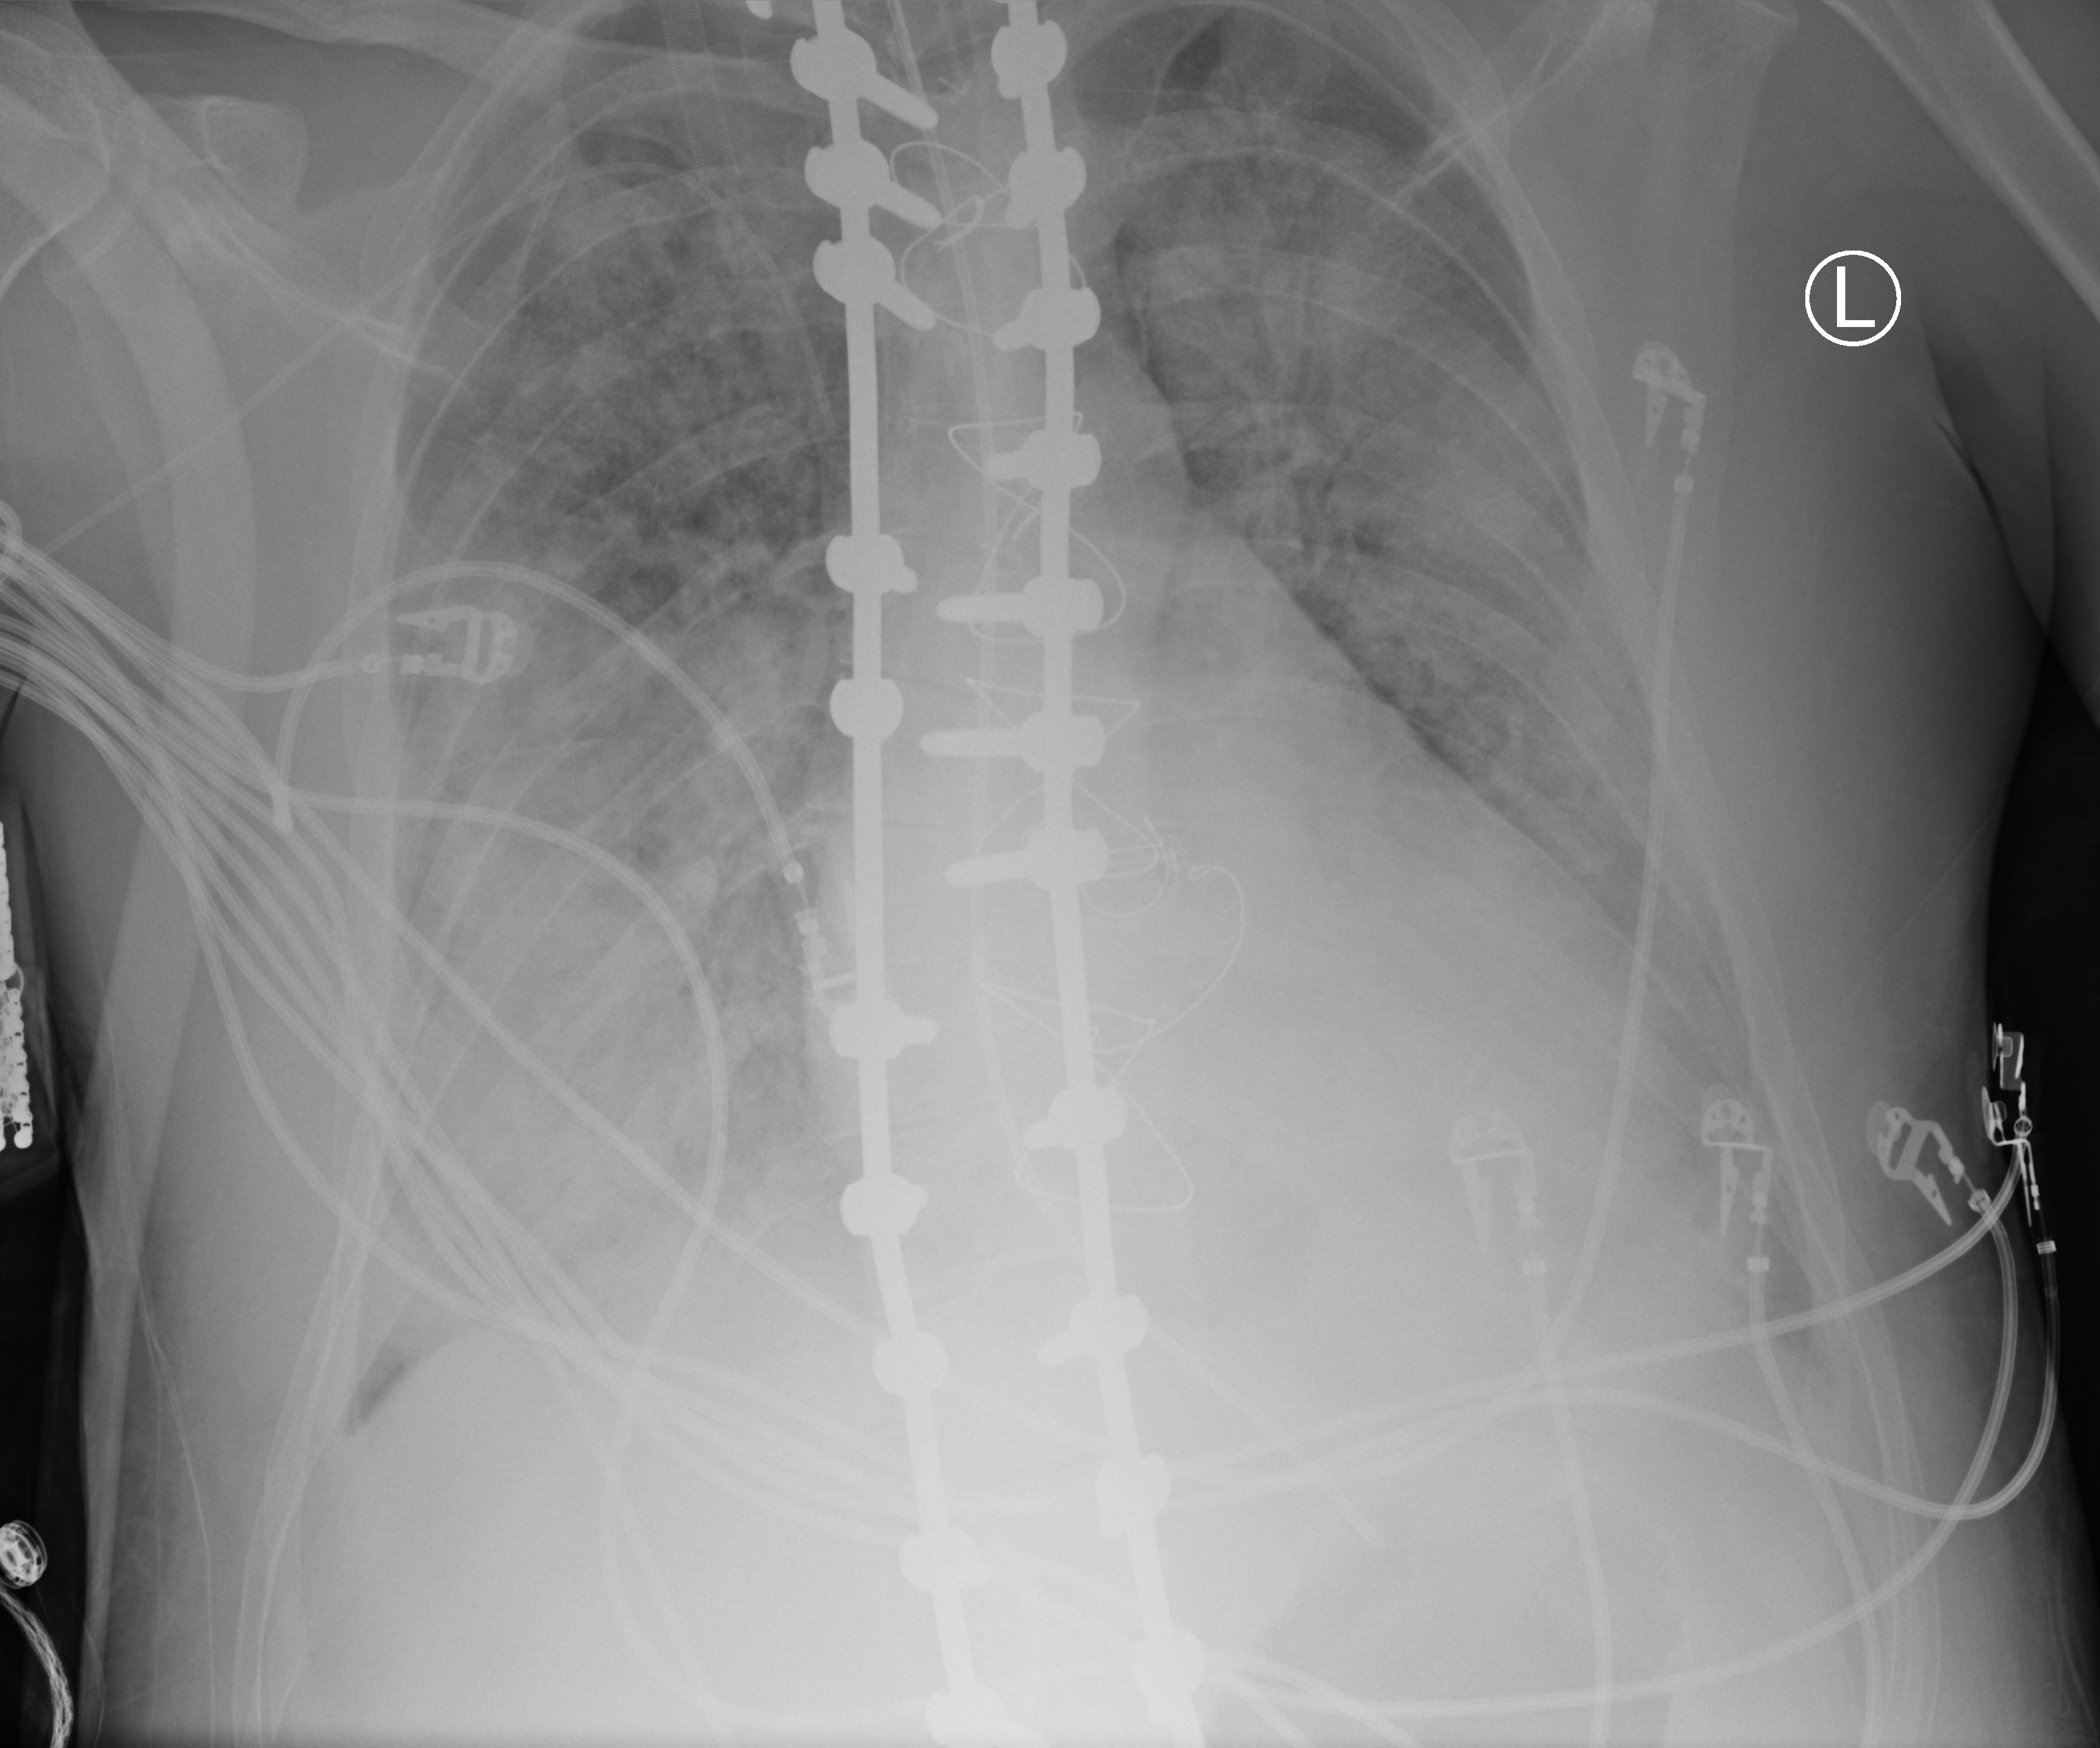
Chest radiograph, anteroposterior (AP) projection. Adult patient hospitalised with COVID-19, age 18–59 years.
From the hospital-stay record, not from the radiograph (when in the stay this image was taken is not recorded):
- length of hospital stay: 15 days
- diabetes (admission record): no
- admitted to intensive care during this hospital stay: yes